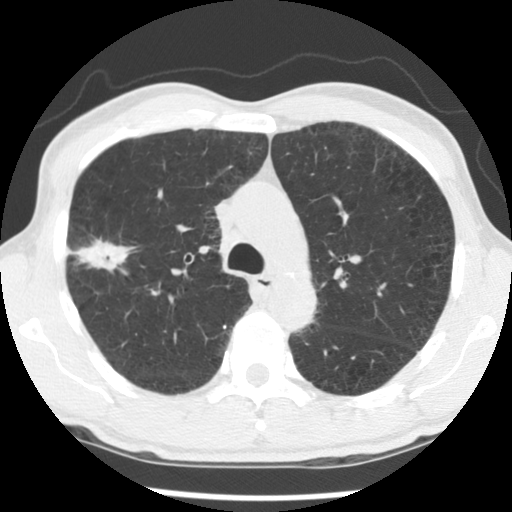
Chest CT (low-dose screening protocol), one axial image, second annual screen, lung window (W 1500 / L -600 HU). Male, age 56 years at enrolment.
Expert-annotated lung lesion, bounding box (x1, y1, x2, y2) in pixels: (54, 231, 140, 294). Screening reader's record for this exam (one nodule recorded; not confirmed to be the boxed lesion): non-calcified nodule or mass ≥4 mm, right upper lobe, 30 × 18 mm, spiculated (stellate) margins, mixed attenuation, pre-existing on the prior screen: yes; interval growth: yes. Official screen result: positive, other. Later outcome: lung cancer diagnosed 326 days after this screen — squamous cell carcinoma, NOS, right upper lobe, right middle lobe, moderately differentiated (G2), stage IB (AJCC 6th edition), 70 mm at pathology.